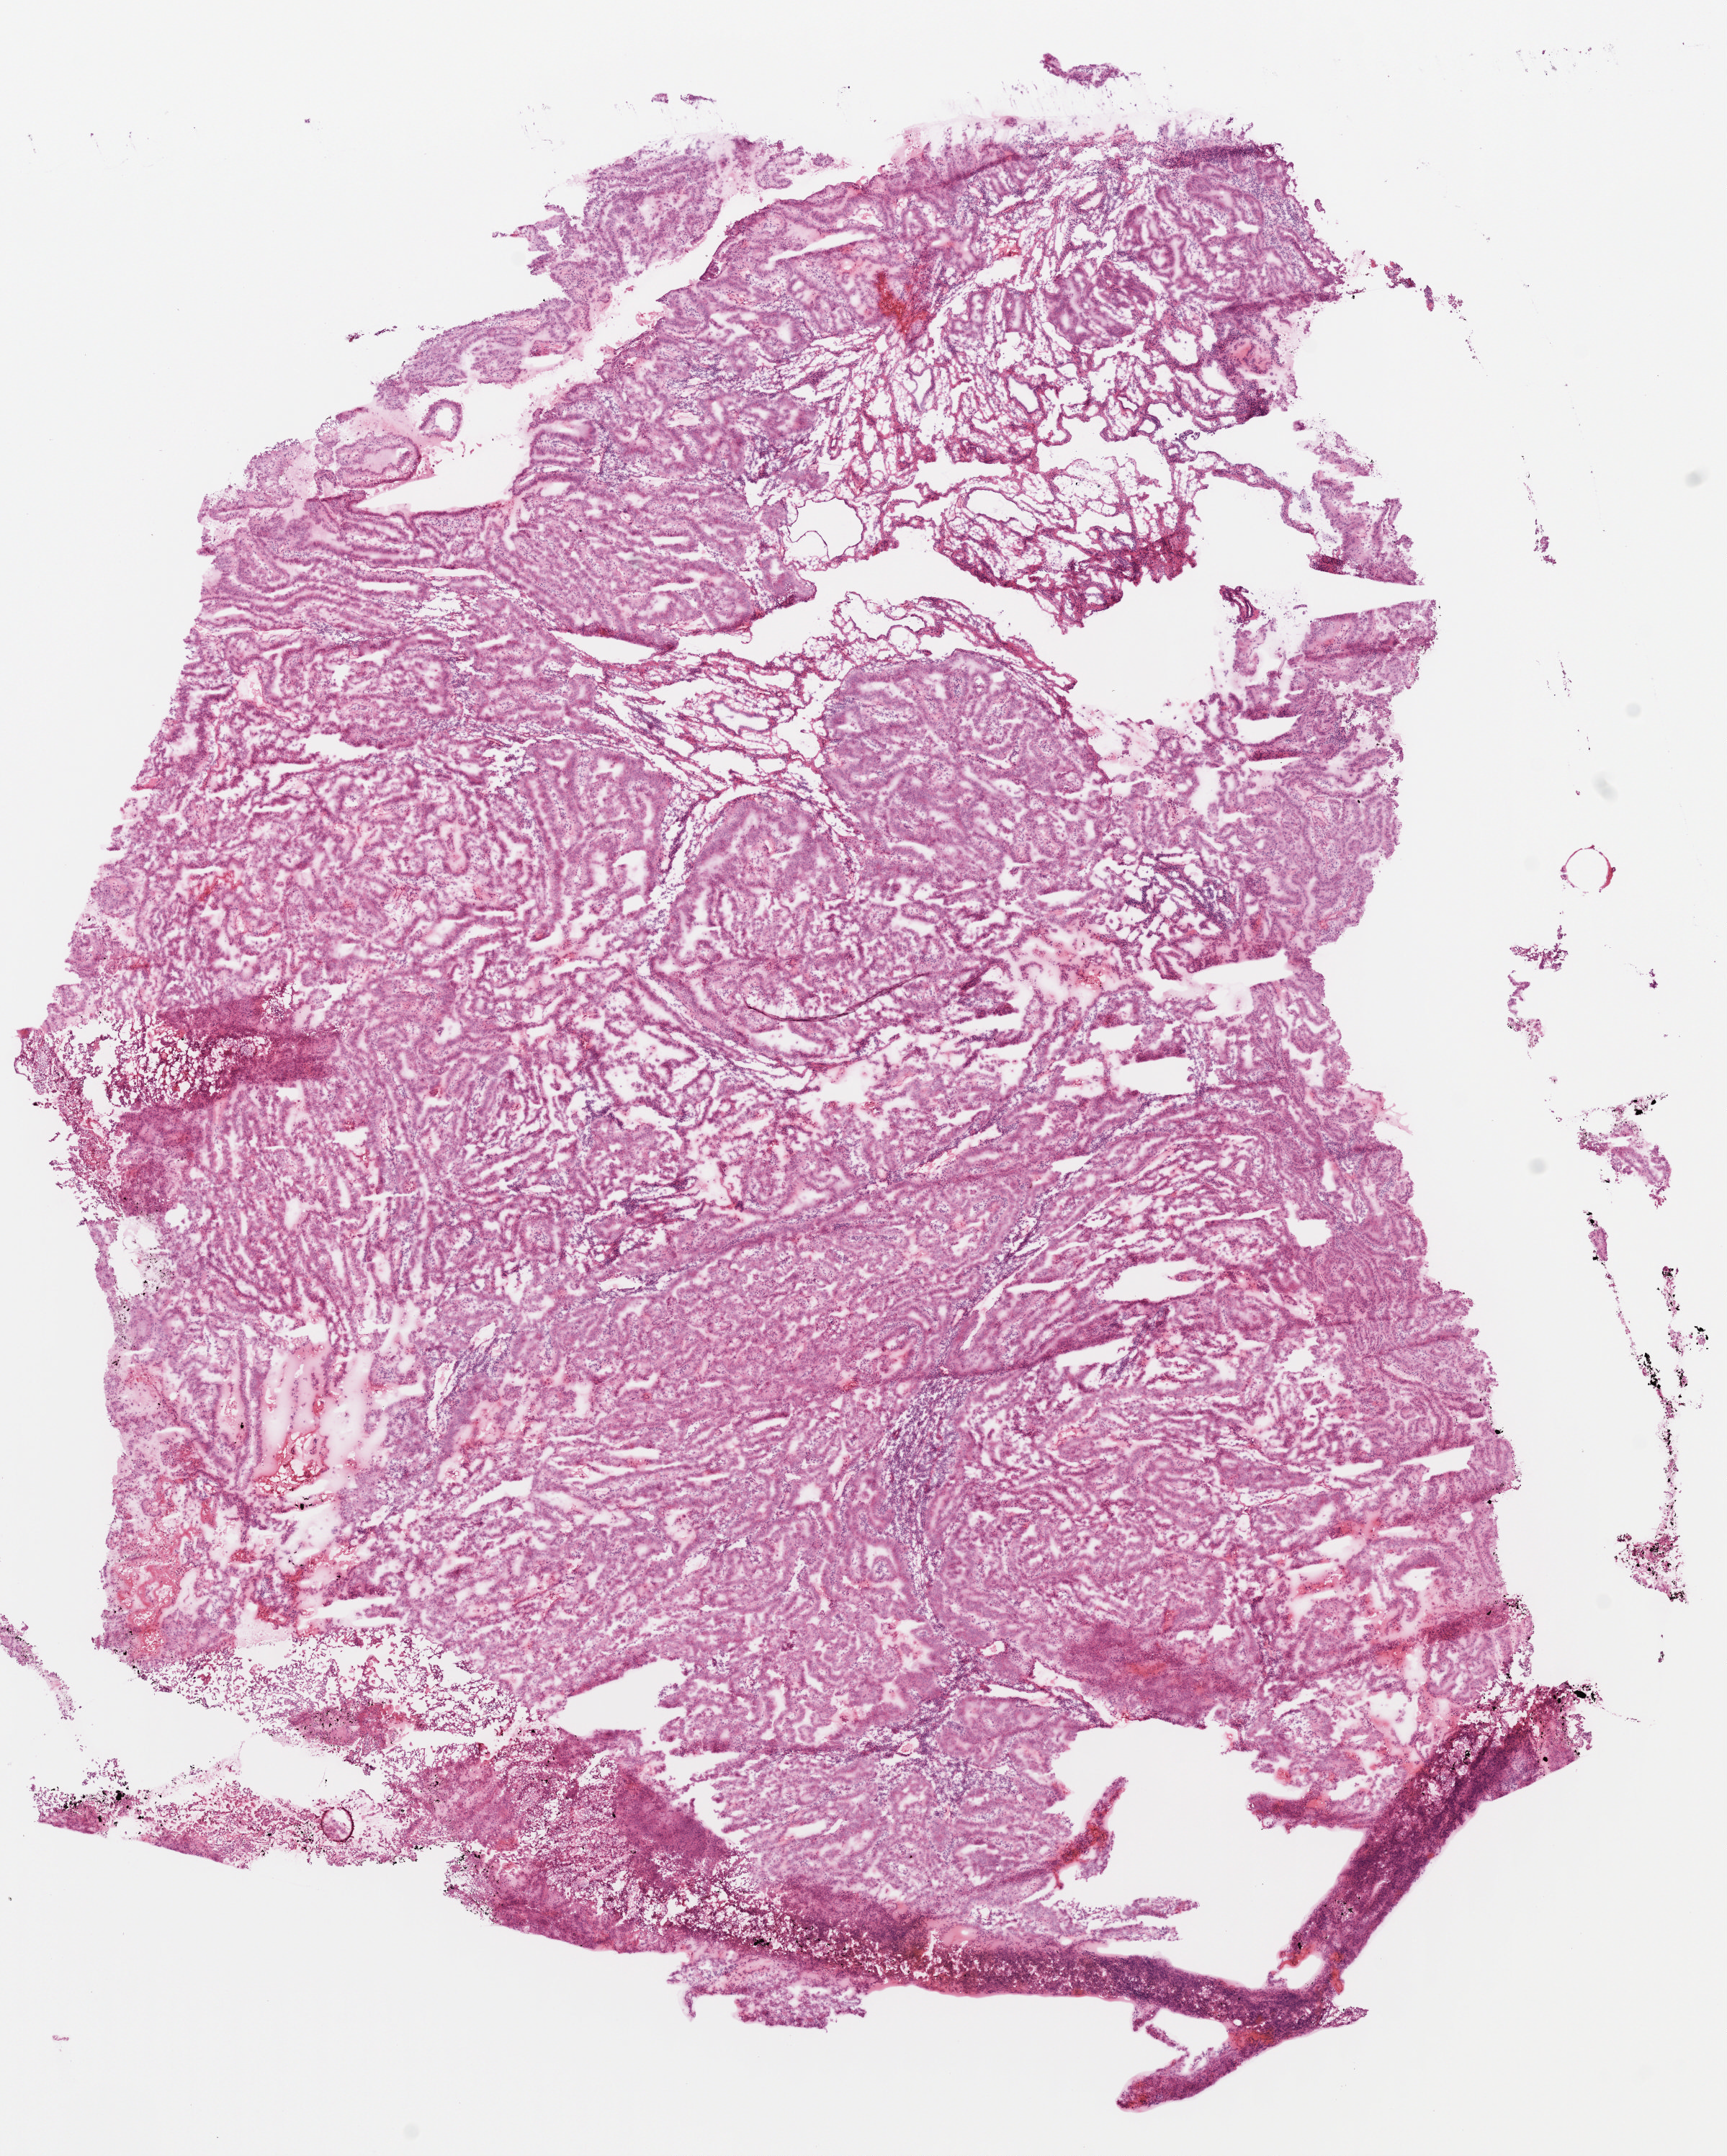
Whole-slide histology image, H&E-stained — whole scanned area (about 9.7 x 12.1 mm, from a 40x scan) shown as a low-resolution overview, frozen section from the top of the tissue portion, uterus, primary tumour sample. Female patient; age at initial diagnosis 64 years. Histologic grade: G1 (well differentiated). Composition of this section per pathologist review: tumour cells 80%, tumour nuclei 80%, normal cells 10%, stromal cells 10%, necrosis 0%. Infiltration values recorded for this section: lymphocyte infiltration 5%, monocyte infiltration 0%, neutrophil infiltration 5%.
FIGO stage: II. Histologic diagnosis: Endometrioid adenocarcinoma, NOS (endometrium).